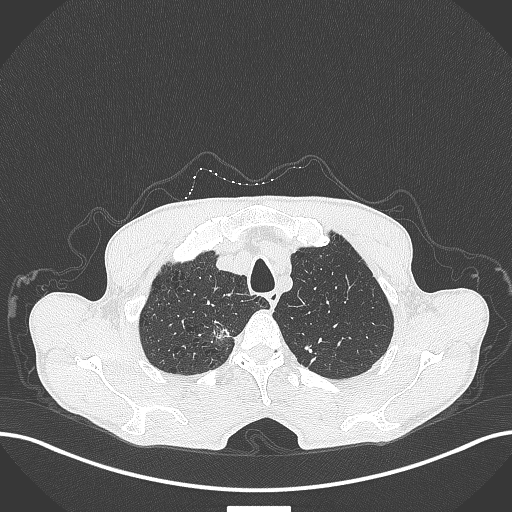
Chest CT, one axial slice; position 369 of 445 along the scan axis; reconstruction kernel B70f; lung window (W 1500 / L -600 HU); 1 mm slice thickness; 512 × 512 image matrix, field of view 400 × 400 mm. Male patient, age 70 years. Case-level facts recorded for this patient, not image findings: clinical TNM (as recorded): T1a N0 M0; histopathological grade: G1-2.
Outlined on this slice (rectangle marked by the reading radiologist):
- lung tumour (recorded histology: adenocarcinoma): box from (x=211, y=317) to (x=240, y=344) px